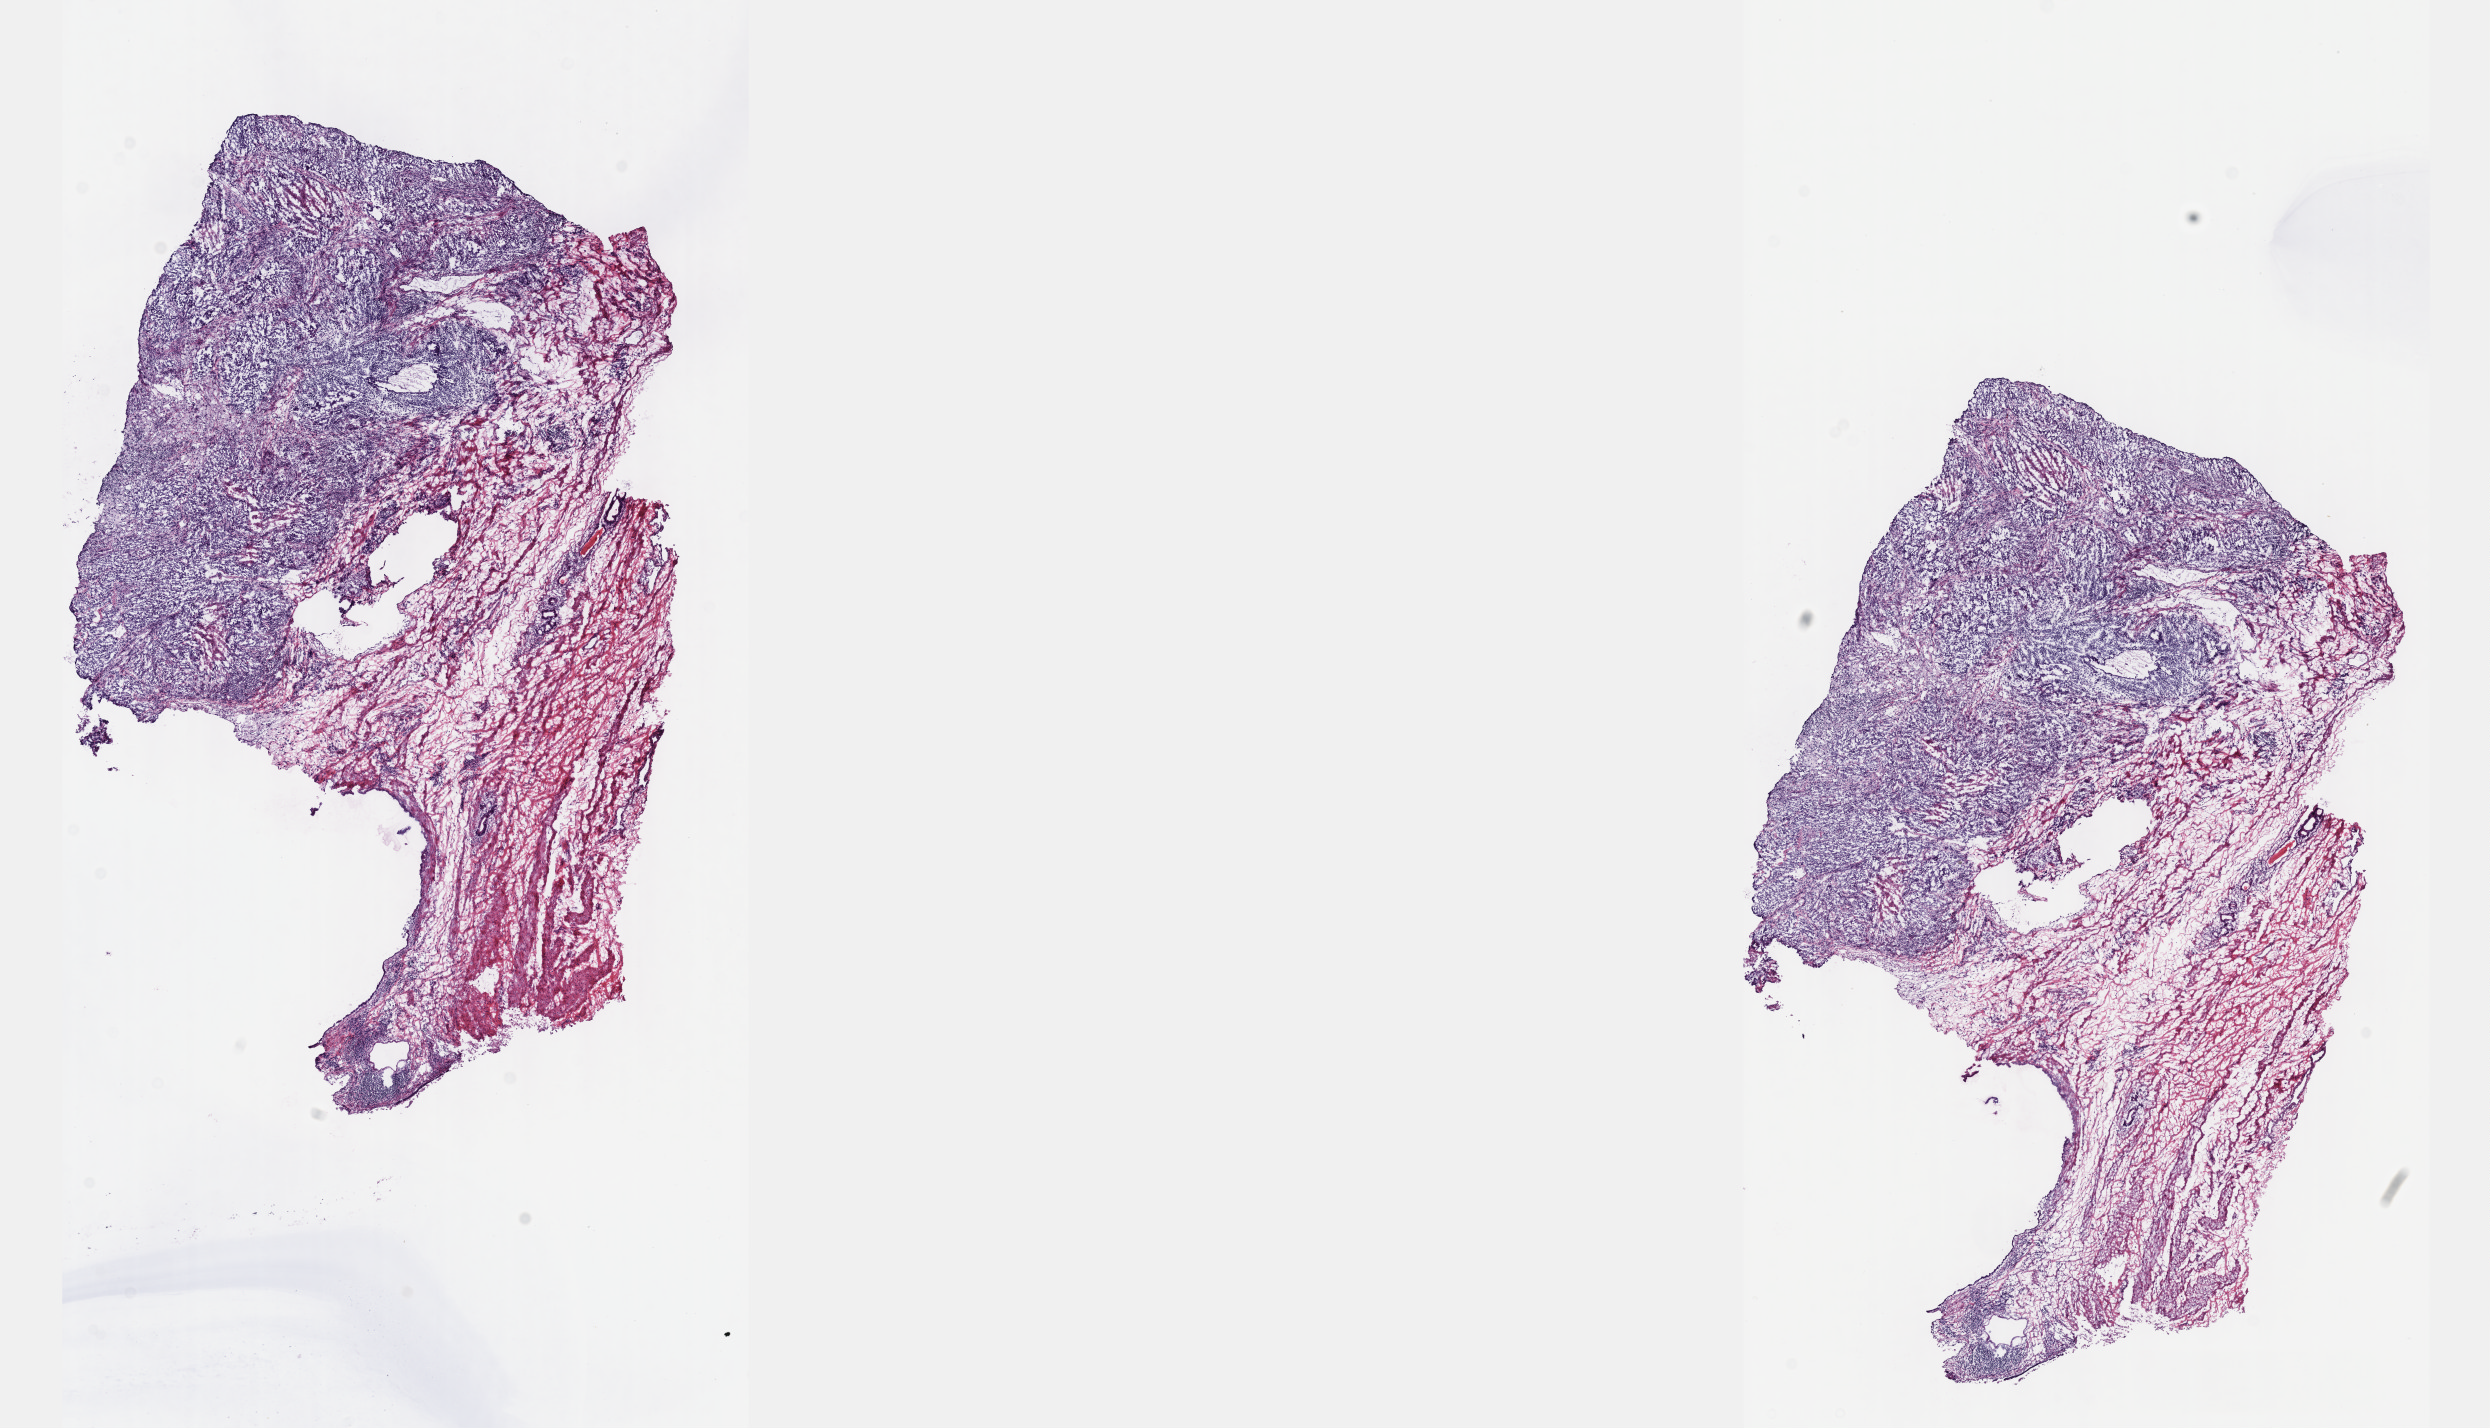
H&E whole-slide image — whole scanned area (about 20.1 x 11.5 mm) shown as a low-resolution overview, frozen section from the top of the tissue portion, sample: primary tumour, testis. Male patient; age at initial diagnosis 43 years. Slide review estimates, as recorded: tumour cells 50%, tumour nuclei 60%, normal cells 50%, stromal cells 0%, necrosis 0%. Inflammatory infiltration, as recorded: lymphocyte infiltration 3%, monocyte infiltration 0%, neutrophil infiltration 0%.
Histologic diagnosis: Mixed germ cell tumor. Laterality: left. AJCC pathologic stage: IIIB (6th edition).